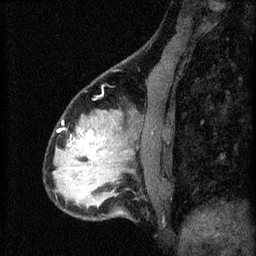
Breast MRI (dynamic contrast-enhanced), one sagittal slice; position 21 of 60 along the scan axis; 3 images stored at this slice position (order not interpretable as contrast timing); 1.5 T; TE 4.2 ms, TR 8.2 ms; 2.3 mm slice thickness; 256 × 256 image matrix. Female patient, age 37 years.
Annotated regions visible in this slice (semi-automatically segmented with operator editing):
- analysis volume of interest (the breast-tissue region the enhancement analysis was run in; not a lesion): bounding box <67,120,122,179> (left, top, right, bottom; pixels)
- tumour enhancement mask (voxels above the 70 % enhancement threshold inside the analysis volume of interest): <70,136,98,145>